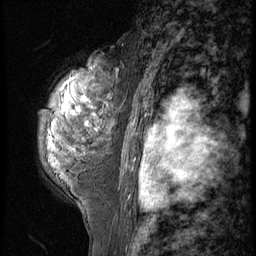
Breast MRI (dynamic contrast-enhanced), one sagittal slice. Slice 39 of 56 in the series (ordered by position). 3 images stored at this slice position (order not interpretable as contrast timing). 1.5 T. TE 4.2 ms, TR 9 ms. 2.5 mm slice thickness. 256 × 256 image matrix, field of view 180 × 180 mm. Female patient, age 50 years. From the clinical record (not read from this slice): setting: breast cancer imaged before/during neoadjuvant chemotherapy; receptor status: triple-negative.
Annotated regions visible in this slice (semi-automatic segmentation, software-assisted and operator-edited):
- analysis volume of interest (the breast-tissue region the enhancement analysis was run in; not a lesion): bounding box <38,50,125,191> (left, top, right, bottom; pixels)
- tumour enhancement mask (voxels above the 140 % enhancement threshold inside the analysis volume of interest): <76,98,97,130>